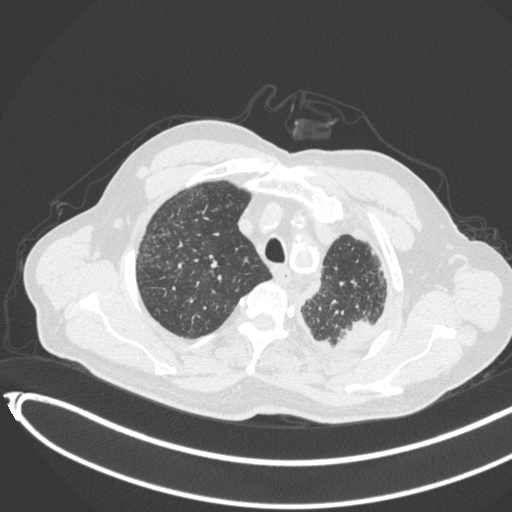
Chest CT, one axial slice; reconstruction kernel B31f; 120 kVp; lung window (W 1500 / L -600 HU); 512 × 512 image matrix, field of view 400 × 400 mm. Patient: male, 78 years. From the clinical record (not read from this slice): clinical TNM (as recorded): T1c N0 M1.
Outlined on this slice (bounding box drawn by a radiologist):
- lung tumour (recorded histology: adenocarcinoma): bounding box <339,314,377,350> (left, top, right, bottom; pixels)